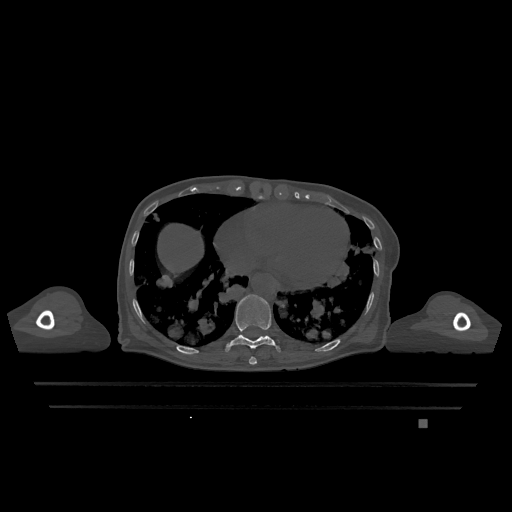
CT including the spine, one axial slice; position 642 of 1317 along the scan axis; bone window (W 1800 / L 400 HU); 512 × 512 image matrix, field of view 500 × 500 mm. Patient: female, 74 years. From the clinical record (not read from this slice): primary cancer: lung.
Structures marked on this image (semi-automatically segmented with operator editing):
- T10 vertebra: bounding box <225,294,281,353> (left, top, right, bottom; pixels)
- T9 vertebra: <249,356,257,365>